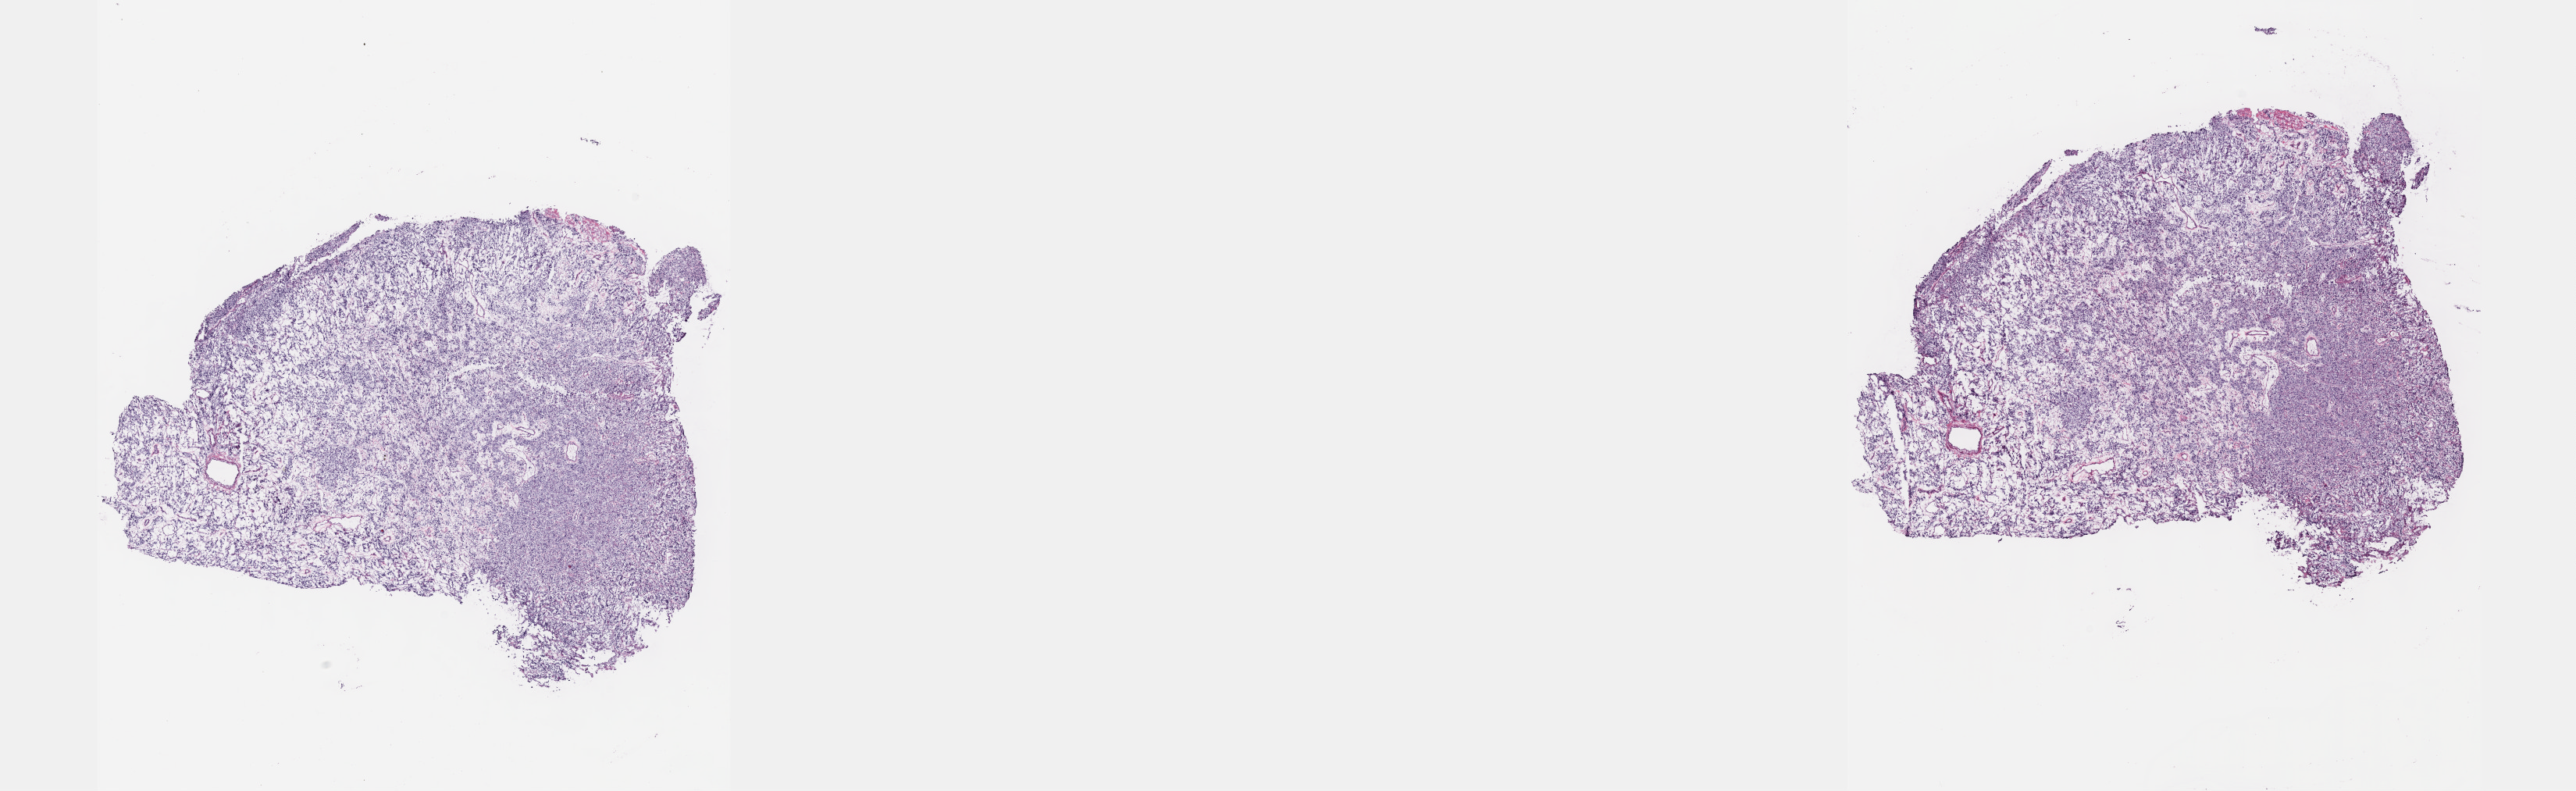
Digitized Hematoxylin and eosin (H&E) stained tissue section (whole slide), a low-resolution overview of the entire scanned area, about 26.7 x 8.2 mm (acquisition: 40x scan), frozen section, retroperitoneum and peritoneum, primary tumour sample. Patient: female, age at initial diagnosis 35 years.
Histologic diagnosis: Extra-adrenal paraganglioma, malignant (retroperitoneum).